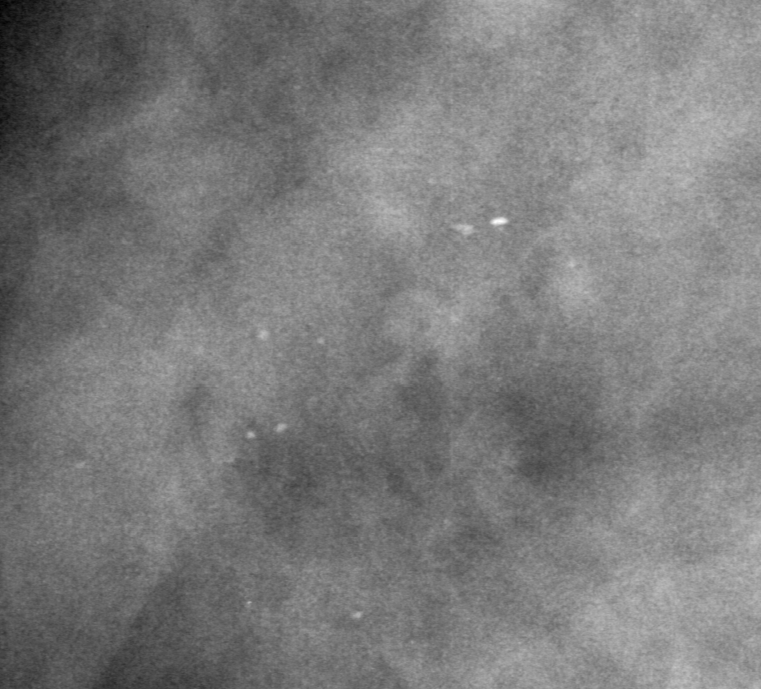
Cropped region of a digitized screen-film mammogram centred on a radiologist-marked abnormality; left breast; MLO view; BI-RADS breast density category 4 (scale 1–4).
- Calcifications, morphology pleomorphic, distribution linear; BI-RADS assessment category 4; subtlety rating 4 on a 1 (subtle) to 5 (obvious) scale; pathology (as recorded): benign.